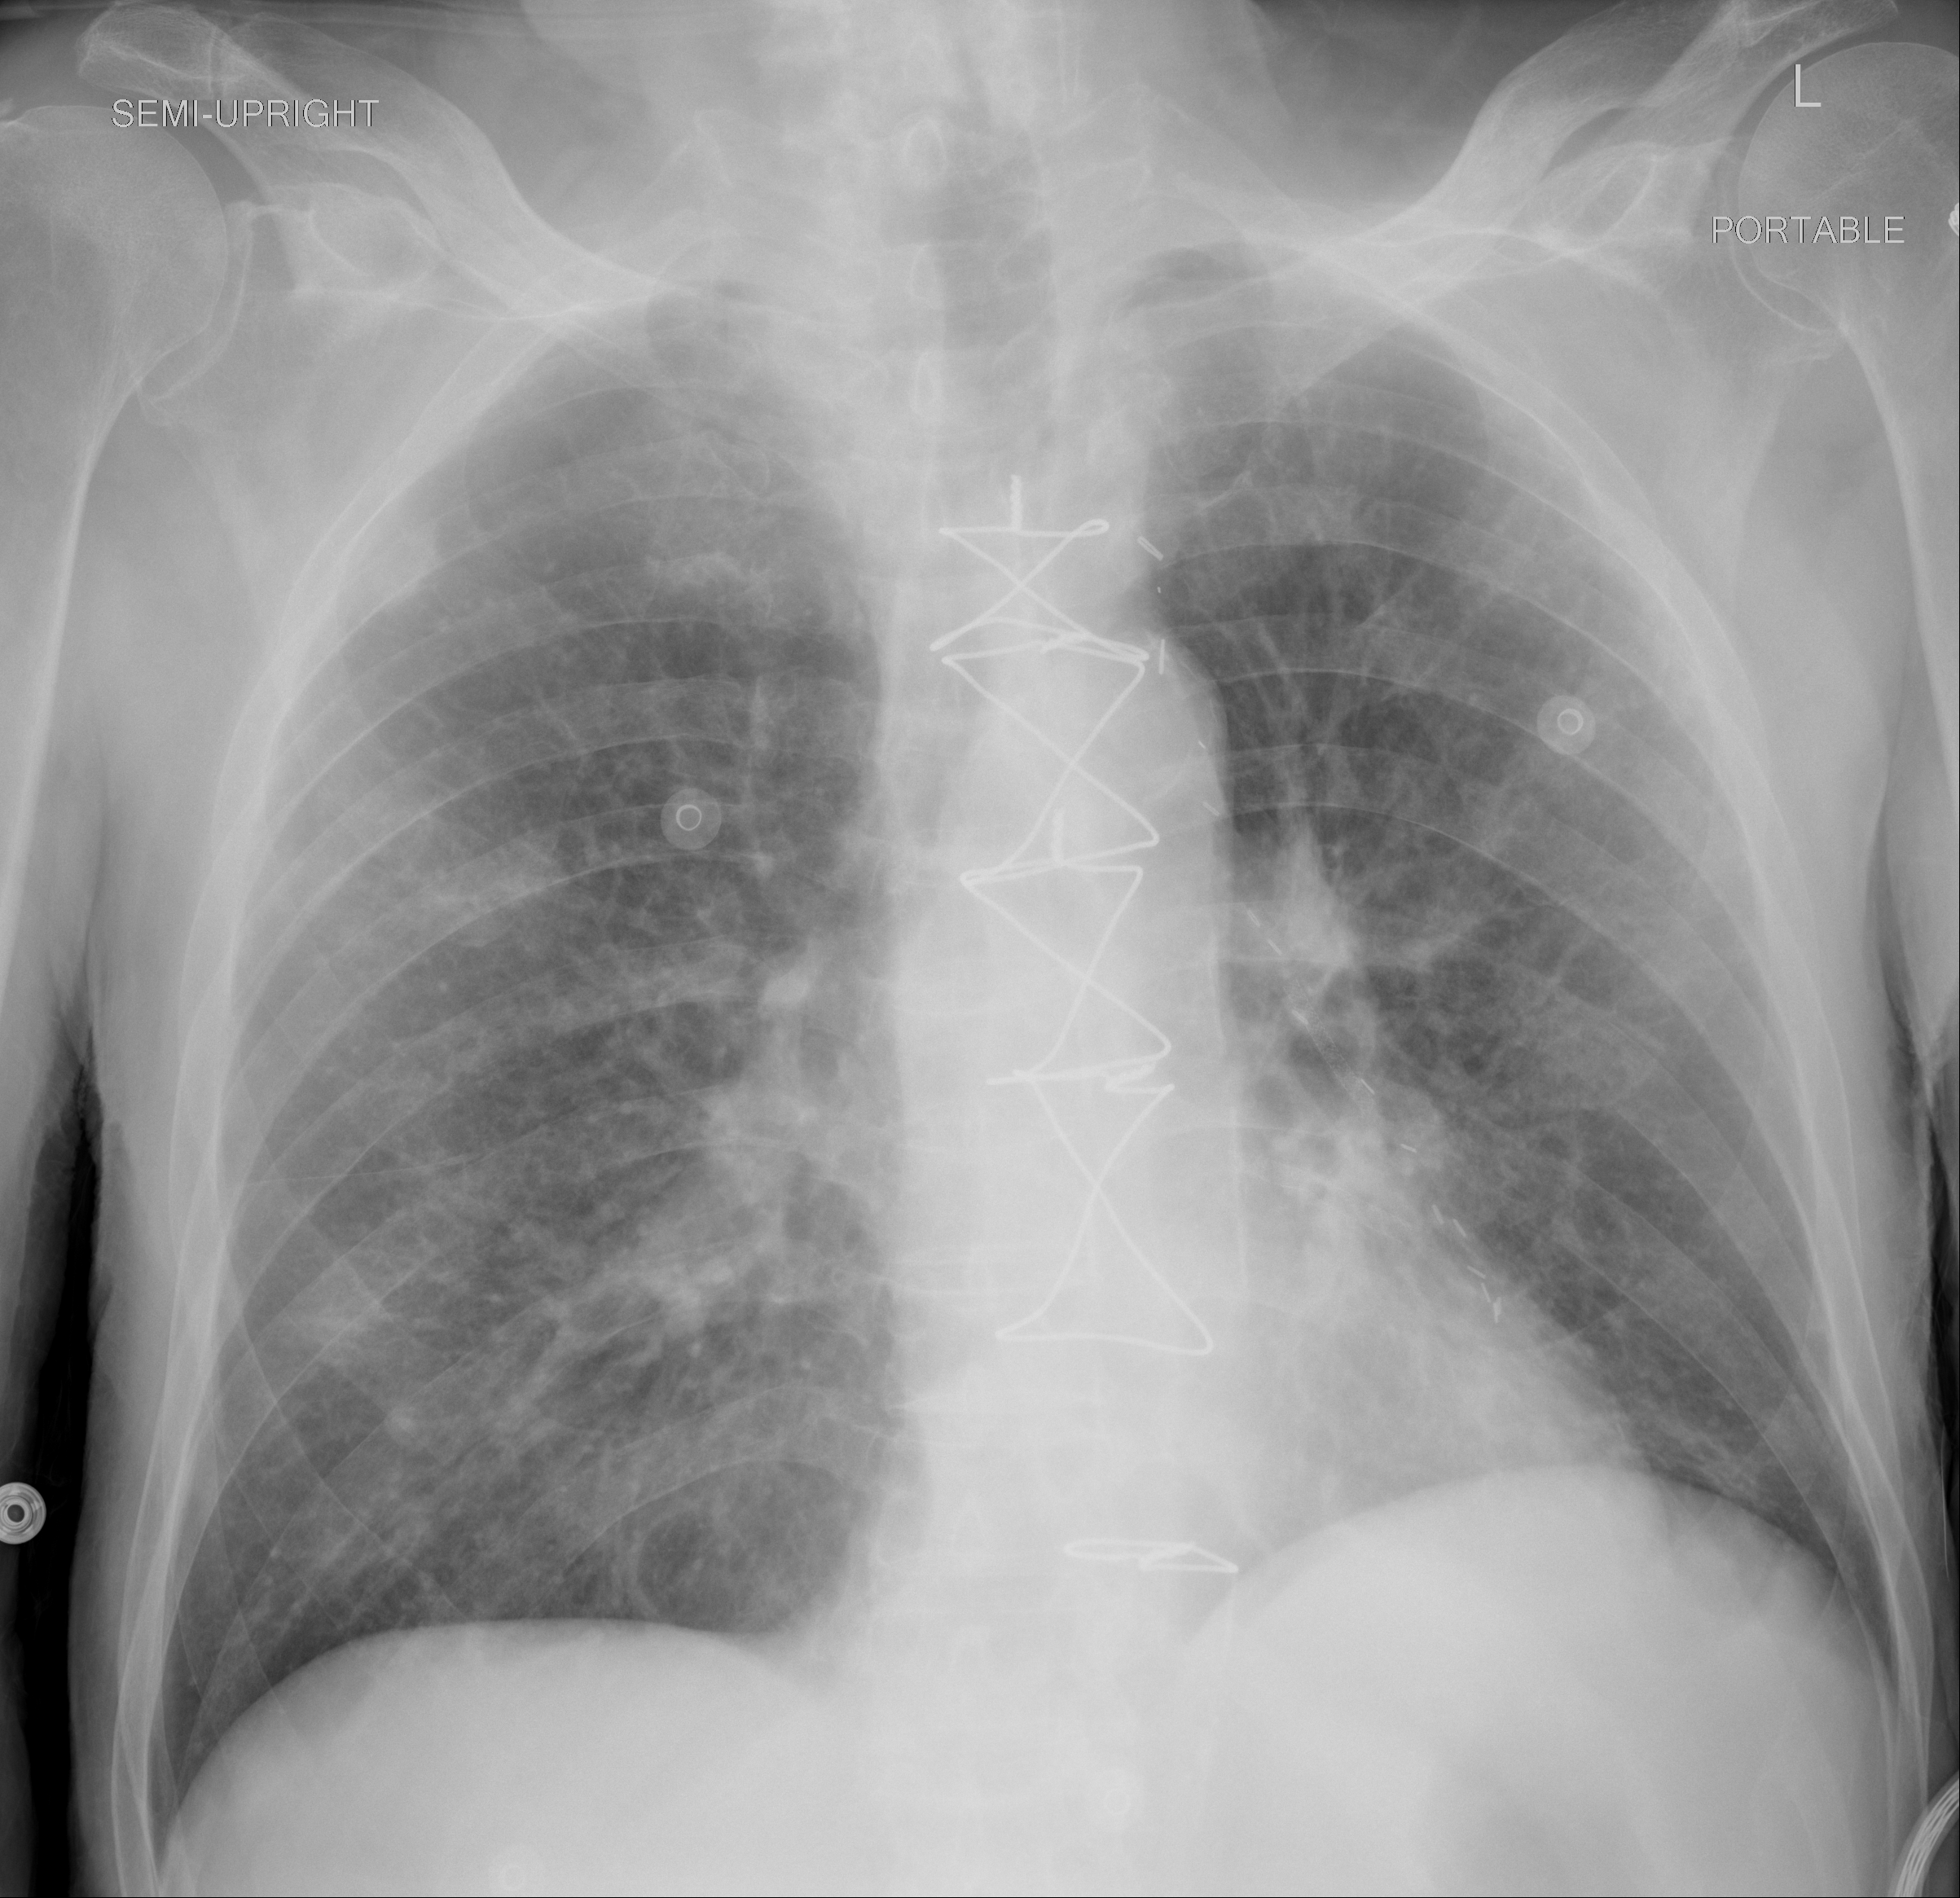
Chest X-ray (portable), AP projection. Male patient, age 81 years; imaged 1 day after the COVID-19 diagnosis.
Radiologist's key findings for this exam: worsening patchy multifocal airspace opacities mainly in the mid to lower lungs bilaterally.